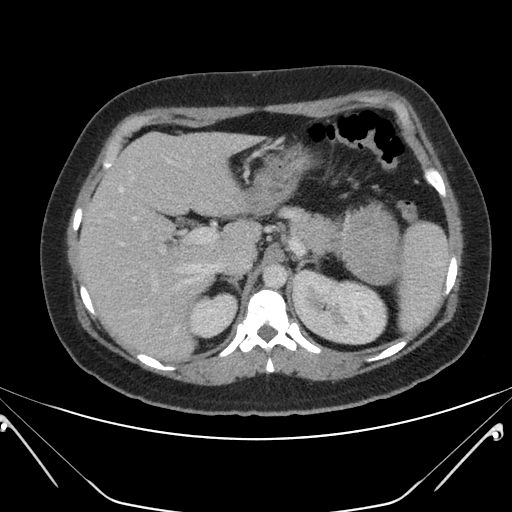
Contrast-enhanced abdominal CT, one axial slice; slice 131 of 168 in the series (ordered by position); intravenous contrast given; soft-tissue window (W 400 / L 40 HU); 512 × 512 image matrix, field of view 394 × 394 mm. Female patient, age 26 years. Case-level facts recorded for this patient, not image findings: diagnosis: adrenocortical carcinoma; tumour side: left adrenal; tumour size at pathology: 28 cm; Ki-67 index: 20 %; stage (as recorded): 2.
Outlined on this slice (semi-automatically segmented with operator editing):
- mass: box from (x=347, y=211) to (x=397, y=283) px